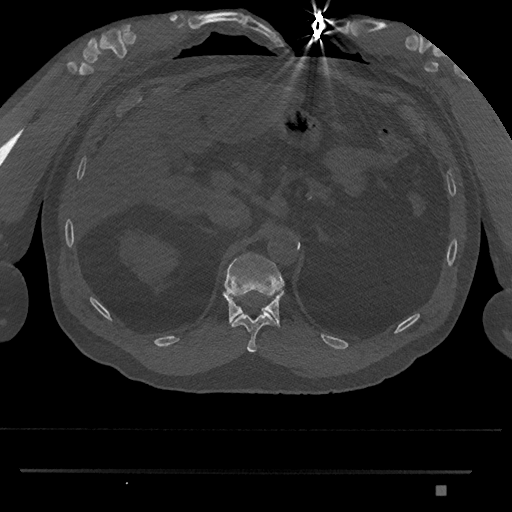
CT including the spine, one axial slice. Slice 918 of 1134 in the series (ordered by position). Reconstruction kernel Br40s/3. 120 kVp. Bone window (W 1800 / L 400 HU). 0.5 mm slice thickness. 512 × 512 image matrix, field of view 429 × 429 mm. Male patient, age 65 years. Case-level facts recorded for this patient, not image findings: primary cancer: prostate.
Outlined on this slice (semi-automatic segmentation, software-assisted and operator-edited):
- T11 vertebra: box from (x=231, y=312) to (x=277, y=353) px
- T12 vertebra: (x=222, y=252)–(x=285, y=328)